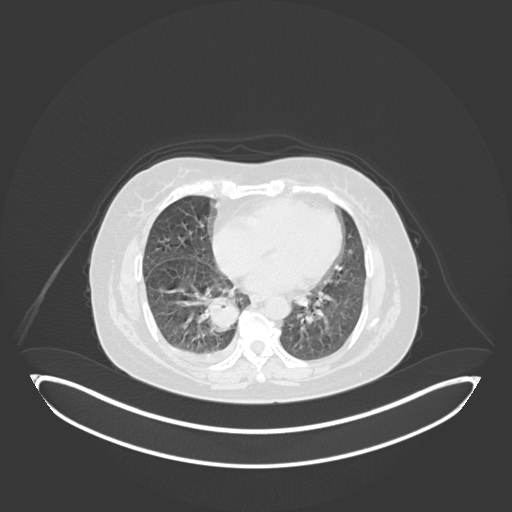
Chest CT, one axial slice; position 59 of 231 along the scan axis; 120 kVp; lung window (W 1500 / L -600 HU); 1 mm slice thickness; 512 × 512 image matrix, field of view 500 × 500 mm. Female patient, age 56 years. Case-level facts recorded for this patient, not image findings: clinical TNM (as recorded): T2b N1 M0.
Annotated regions visible in this slice (rectangle marked by the reading radiologist):
- lung tumour (recorded histology: small cell carcinoma): bounding box (x1, y1, x2, y2) in pixels: (203, 288, 246, 338)